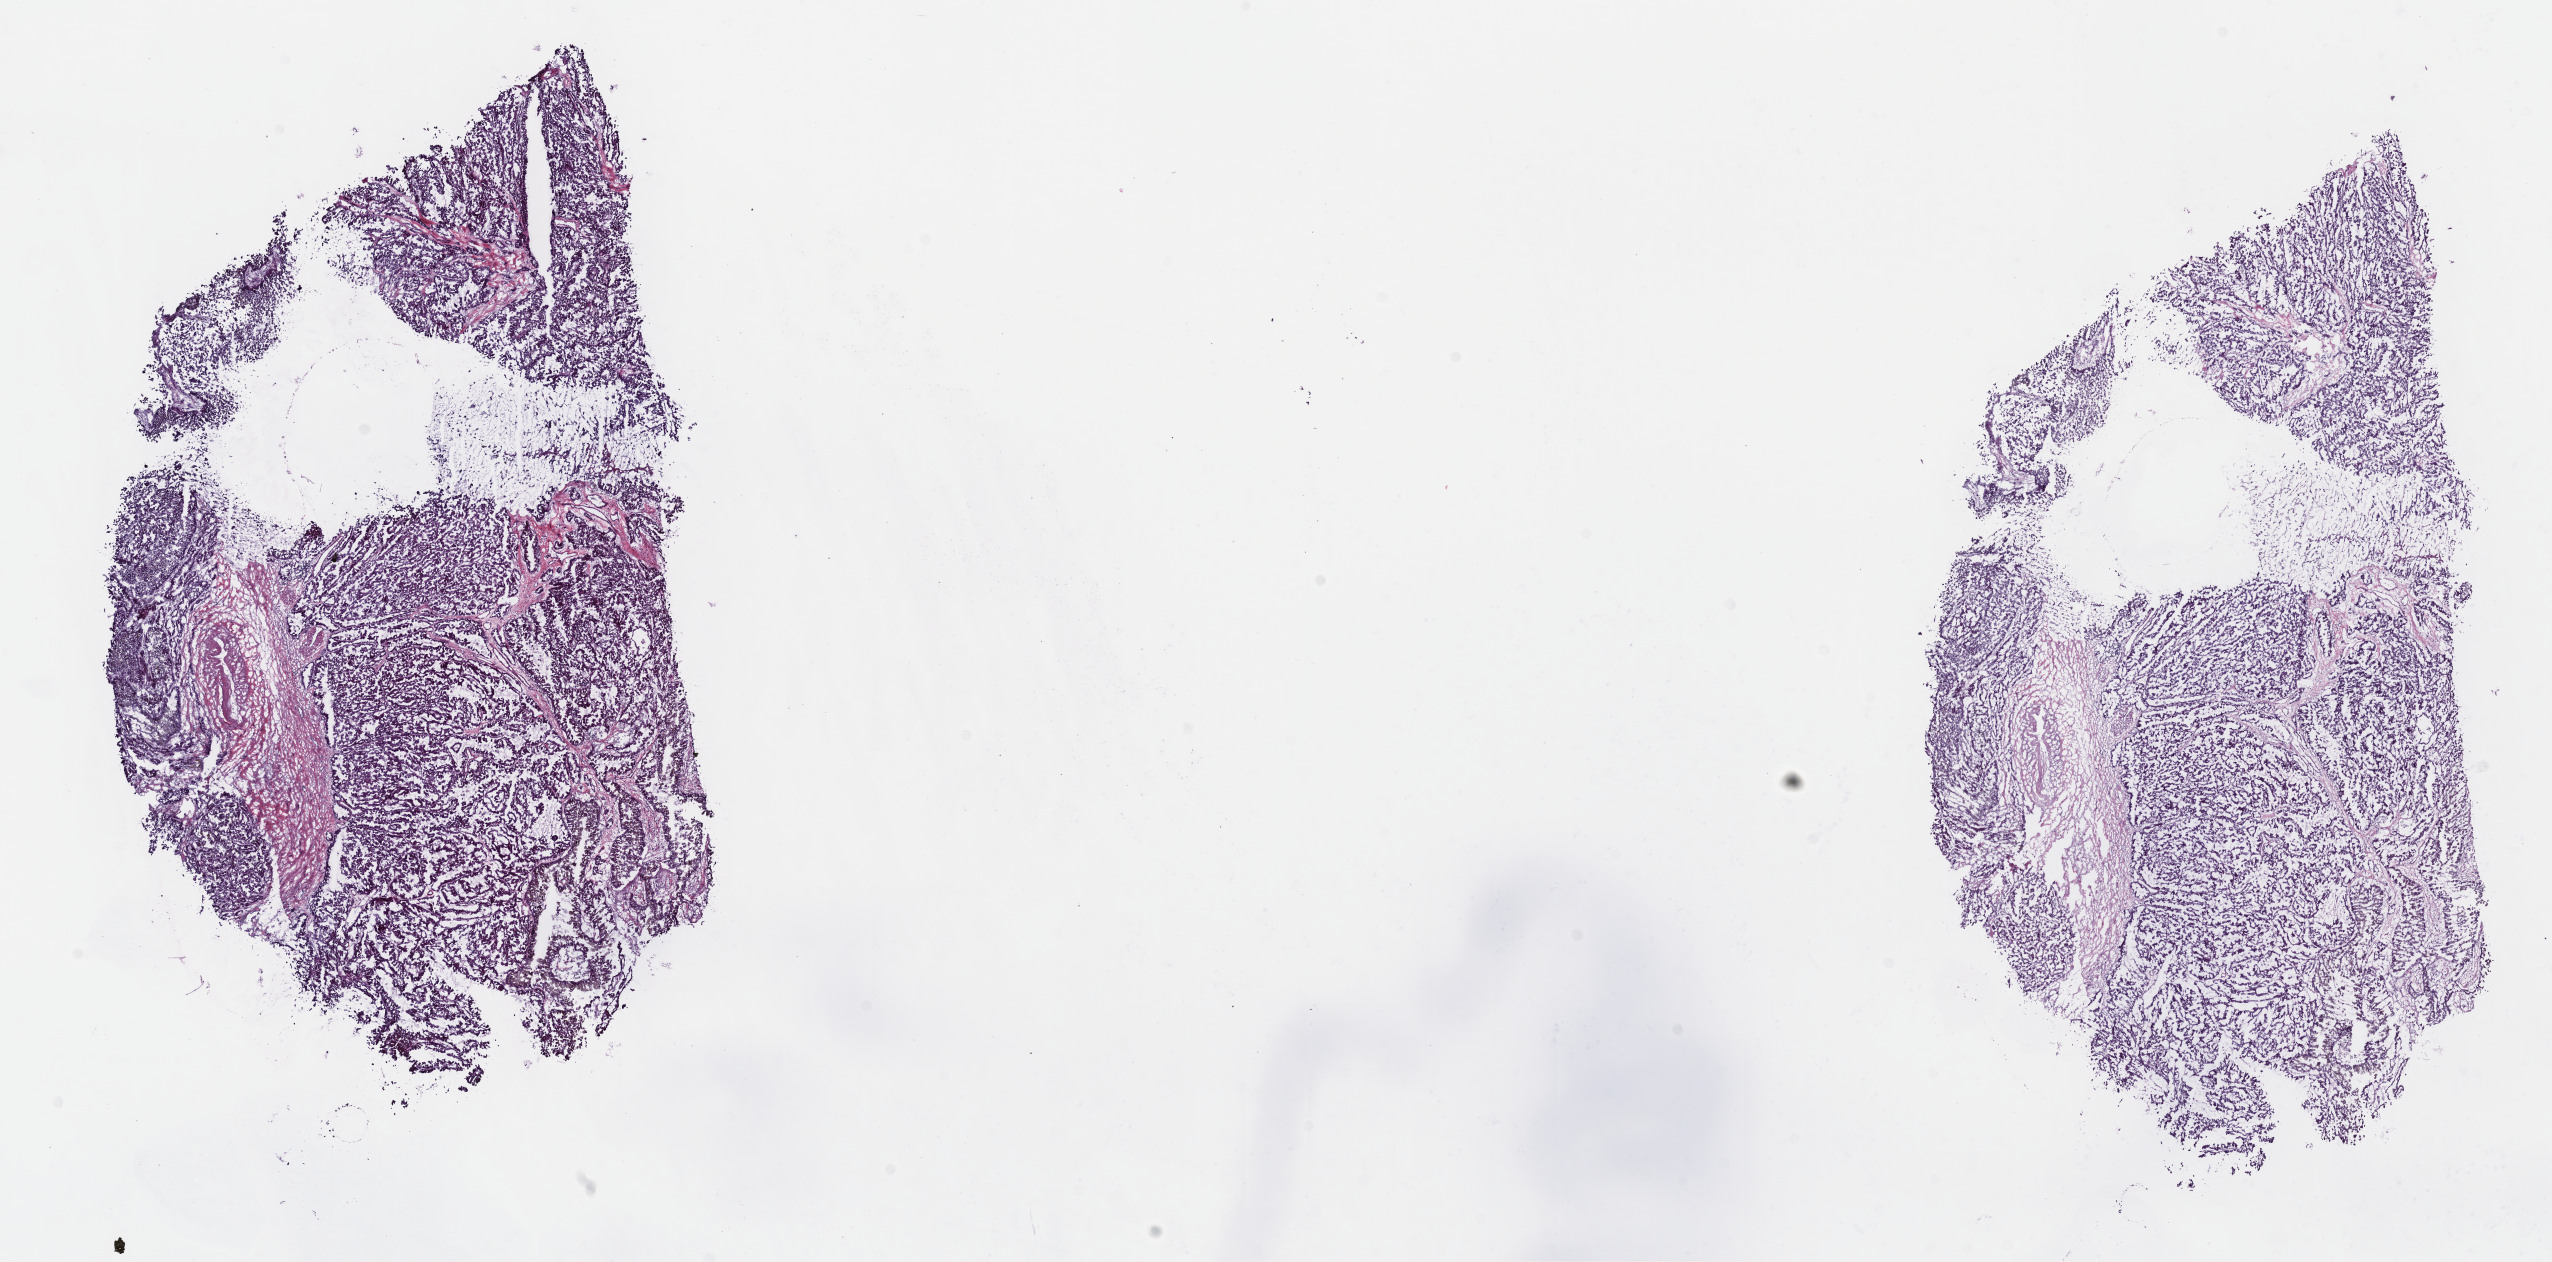
Digitized H&E-stained tissue section (whole slide) — whole scanned area (about 20.6 x 10.2 mm, from a 40x scan) shown as a low-resolution overview, frozen section, primary tumour sample from the kidney. Male, age 74 years at initial diagnosis. Pathologist review of this section (percent, as recorded): tumour cells 75%, tumour nuclei 75%, normal cells 0%, stromal cells 21%, necrosis 4%. Inflammatory infiltration, as recorded: lymphocyte infiltration 2%, monocyte infiltration 5%, neutrophil infiltration 2%.
Laterality: right. AJCC pathologic stage: III (7th edition). Diagnosis: Papillary adenocarcinoma, NOS. TNM: T3a N1 MX. Lymph nodes positive (case pathology): 5 of 7 examined.